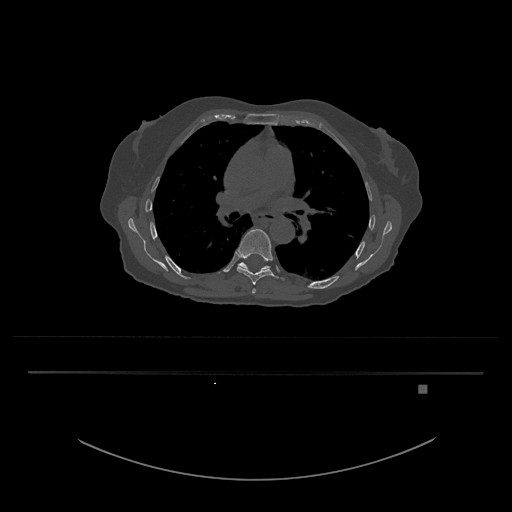
CT including the spine, one axial slice. Slice 796 of 797 in the series (ordered by position). Reconstruction kernel Br40s/3. 120 kVp. Bone window (W 1800 / L 400 HU). 0.5 mm slice thickness. 512 × 512 image matrix, field of view 500 × 500 mm. Female patient, age 57 years. From the clinical record (not read from this slice): primary cancer: cervical.
Structures marked on this image (semi-automatic segmentation, software-assisted and operator-edited):
- T8 vertebra: bounding box (x1, y1, x2, y2) in pixels: (236, 229, 285, 285)
- T9 vertebra: (239, 260, 271, 272)